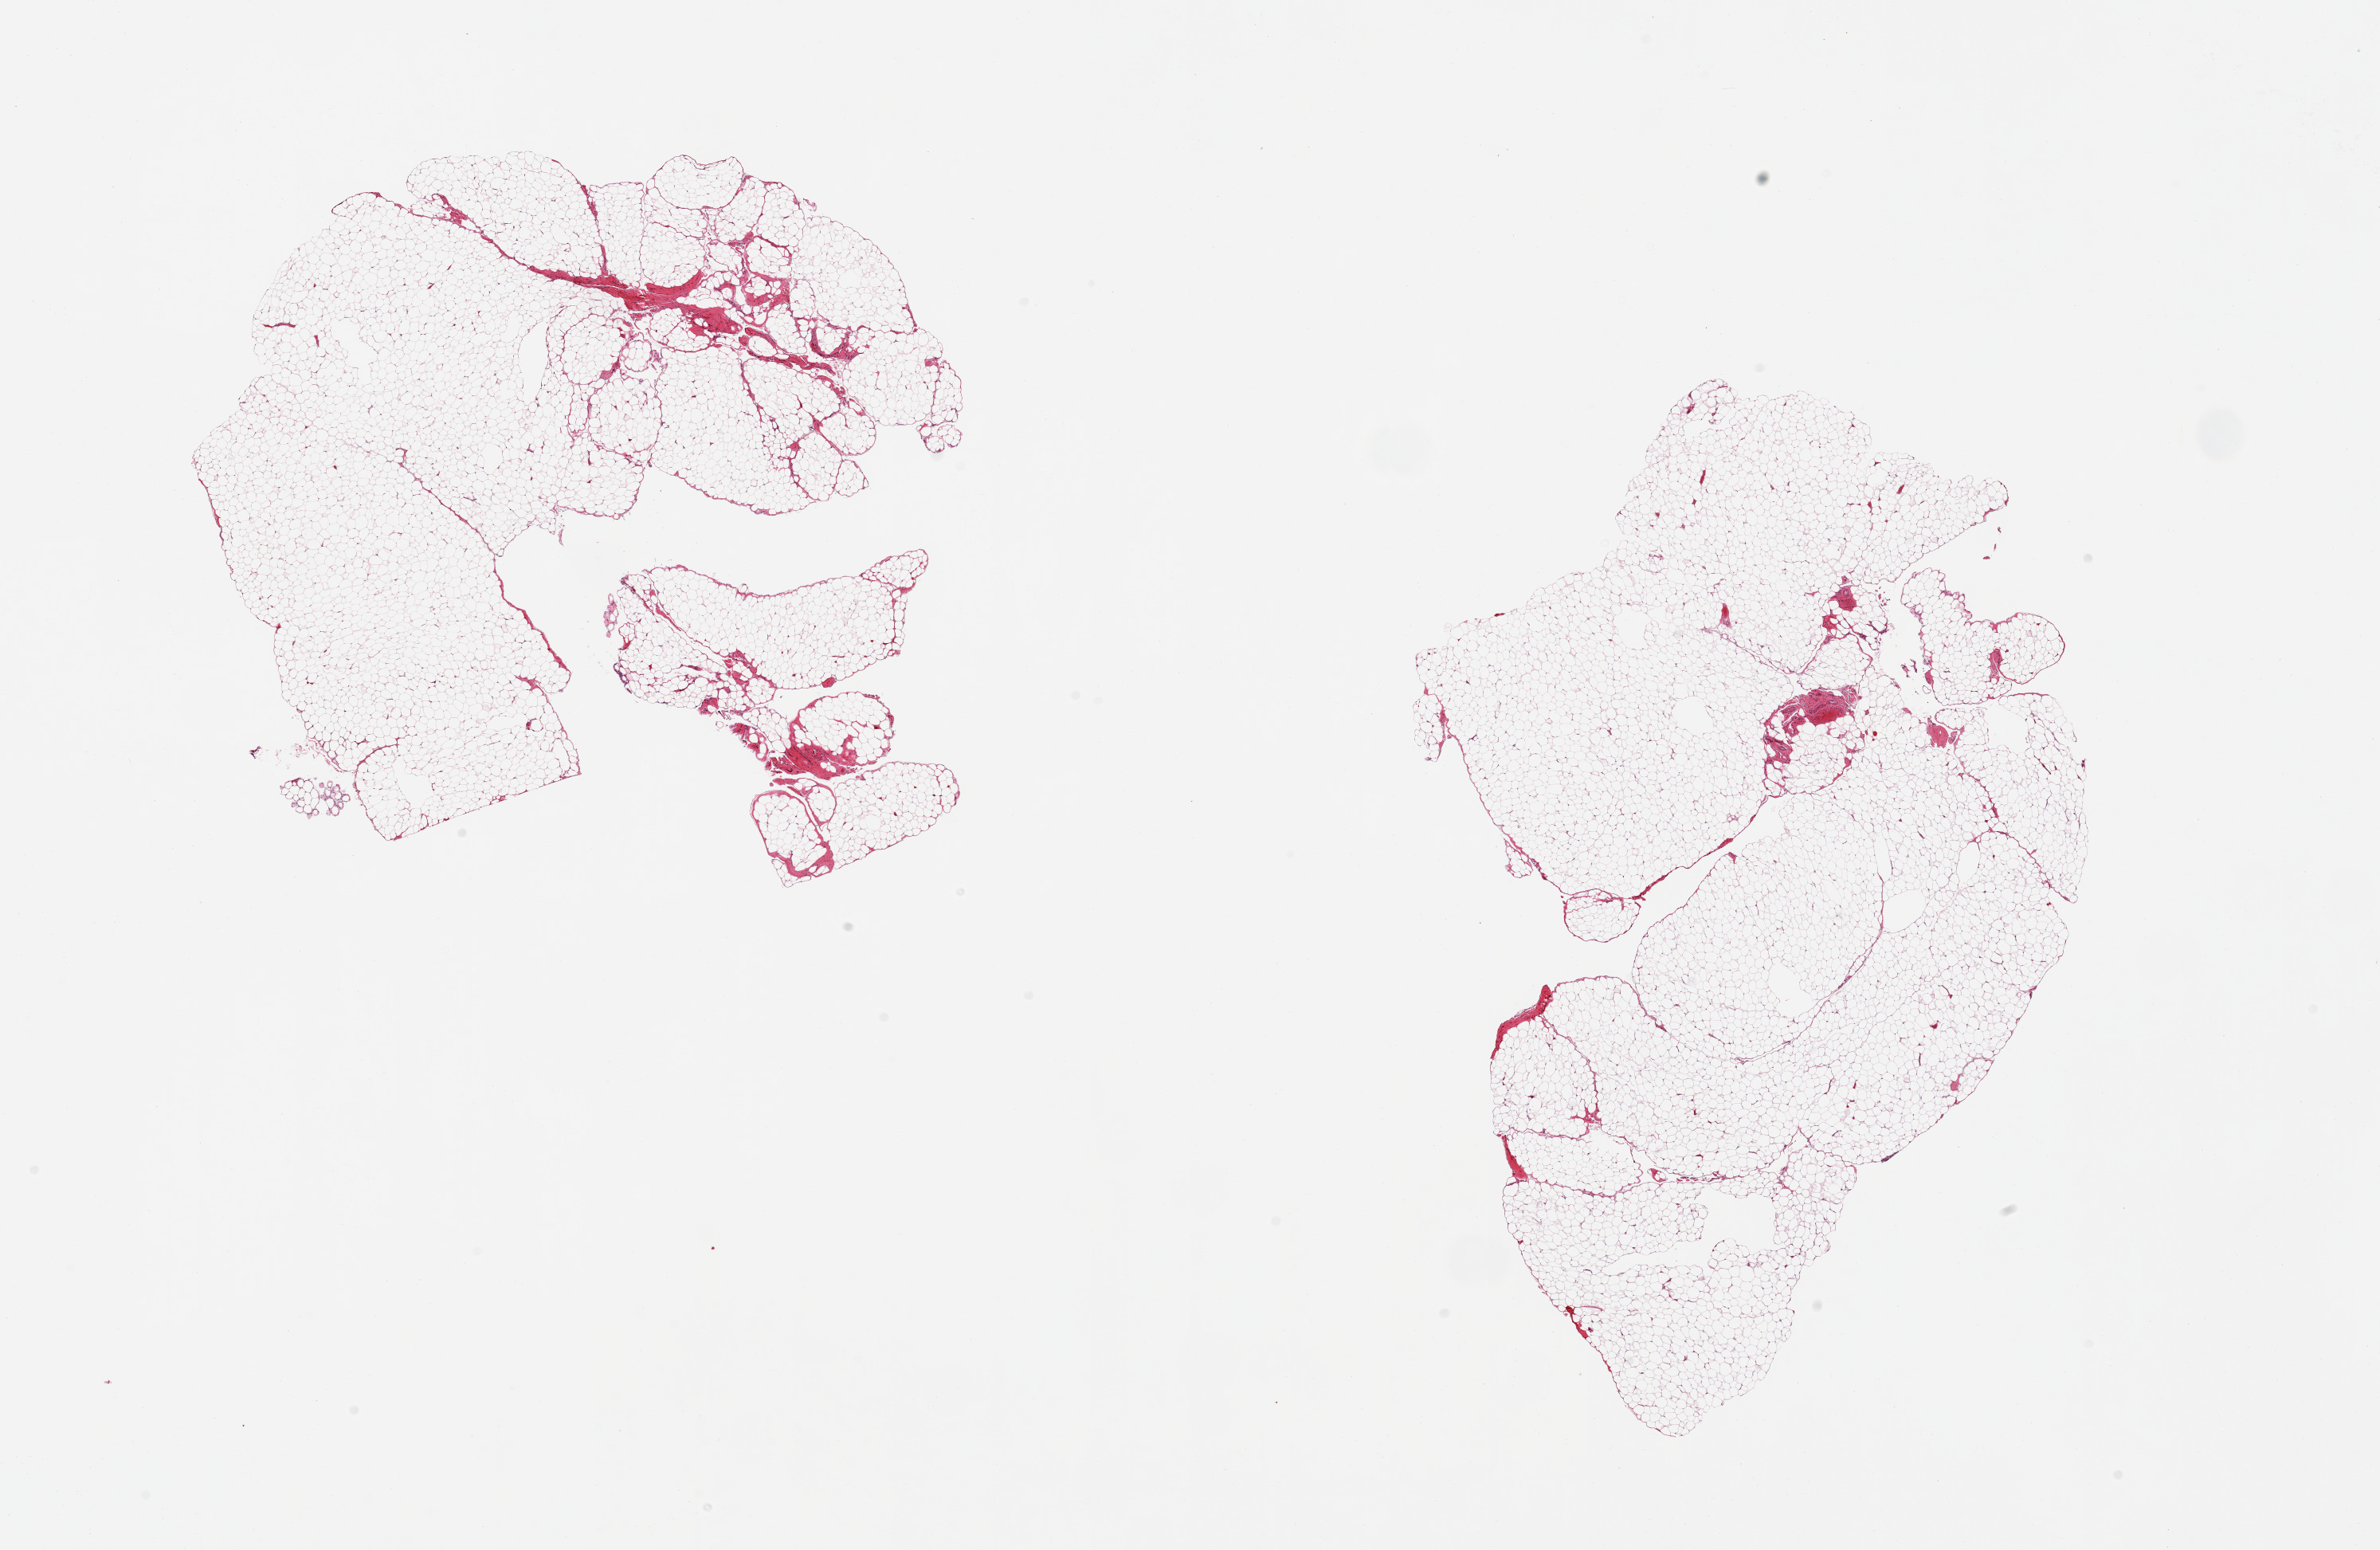
Whole-slide image, hematoxylin and eosin (H&E) stain, whole scanned area (about 23.6 x 15.4 mm) shown as a low-resolution overview. PAXgene-fixed, paraffin-embedded tissue. Target tissue: omentum. Donor tissue sample. Donor sex: male.
- reviewer comment on this tissue sample: 2 pieces